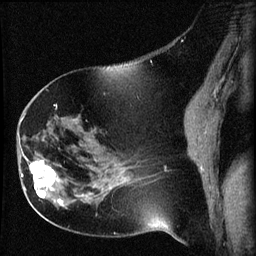
Breast MRI (dynamic contrast-enhanced), one sagittal slice. Position 29 of 60 along the scan axis. Dynamic contrast-enhanced series, image 2 of 3 at this slice position (ordered by acquisition). 1.5 T. TE 4.2 ms, TR 8.2 ms. 2 mm slice thickness. 256 × 256 image matrix, field of view 180 × 180 mm. Patient: female, 63 years.
Structures marked on this image (semi-automatically segmented with operator editing):
- analysis volume of interest (the breast-tissue region the enhancement analysis was run in; not a lesion): box from (x=22, y=156) to (x=64, y=202) px
- tumour enhancement mask (voxels above the 70 % enhancement threshold inside the analysis volume of interest): (x=22, y=158)–(x=63, y=202)